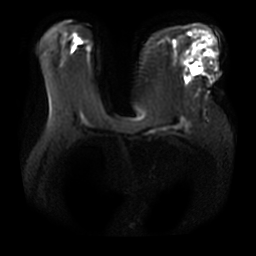
Breast MRI, one axial slice; position 20 of 36 along the scan axis; diffusion-weighted series; image 2 of 4 stored at this slice position (different b-values; order by instance number); 3 T; 5 mm slice thickness; 256 × 256 image matrix, field of view 380 × 380 mm. Female patient.
Annotated regions visible in this slice (outlined manually by an expert reader):
- tumour on diffusion-weighted imaging: box from (x=190, y=64) to (x=201, y=75) px